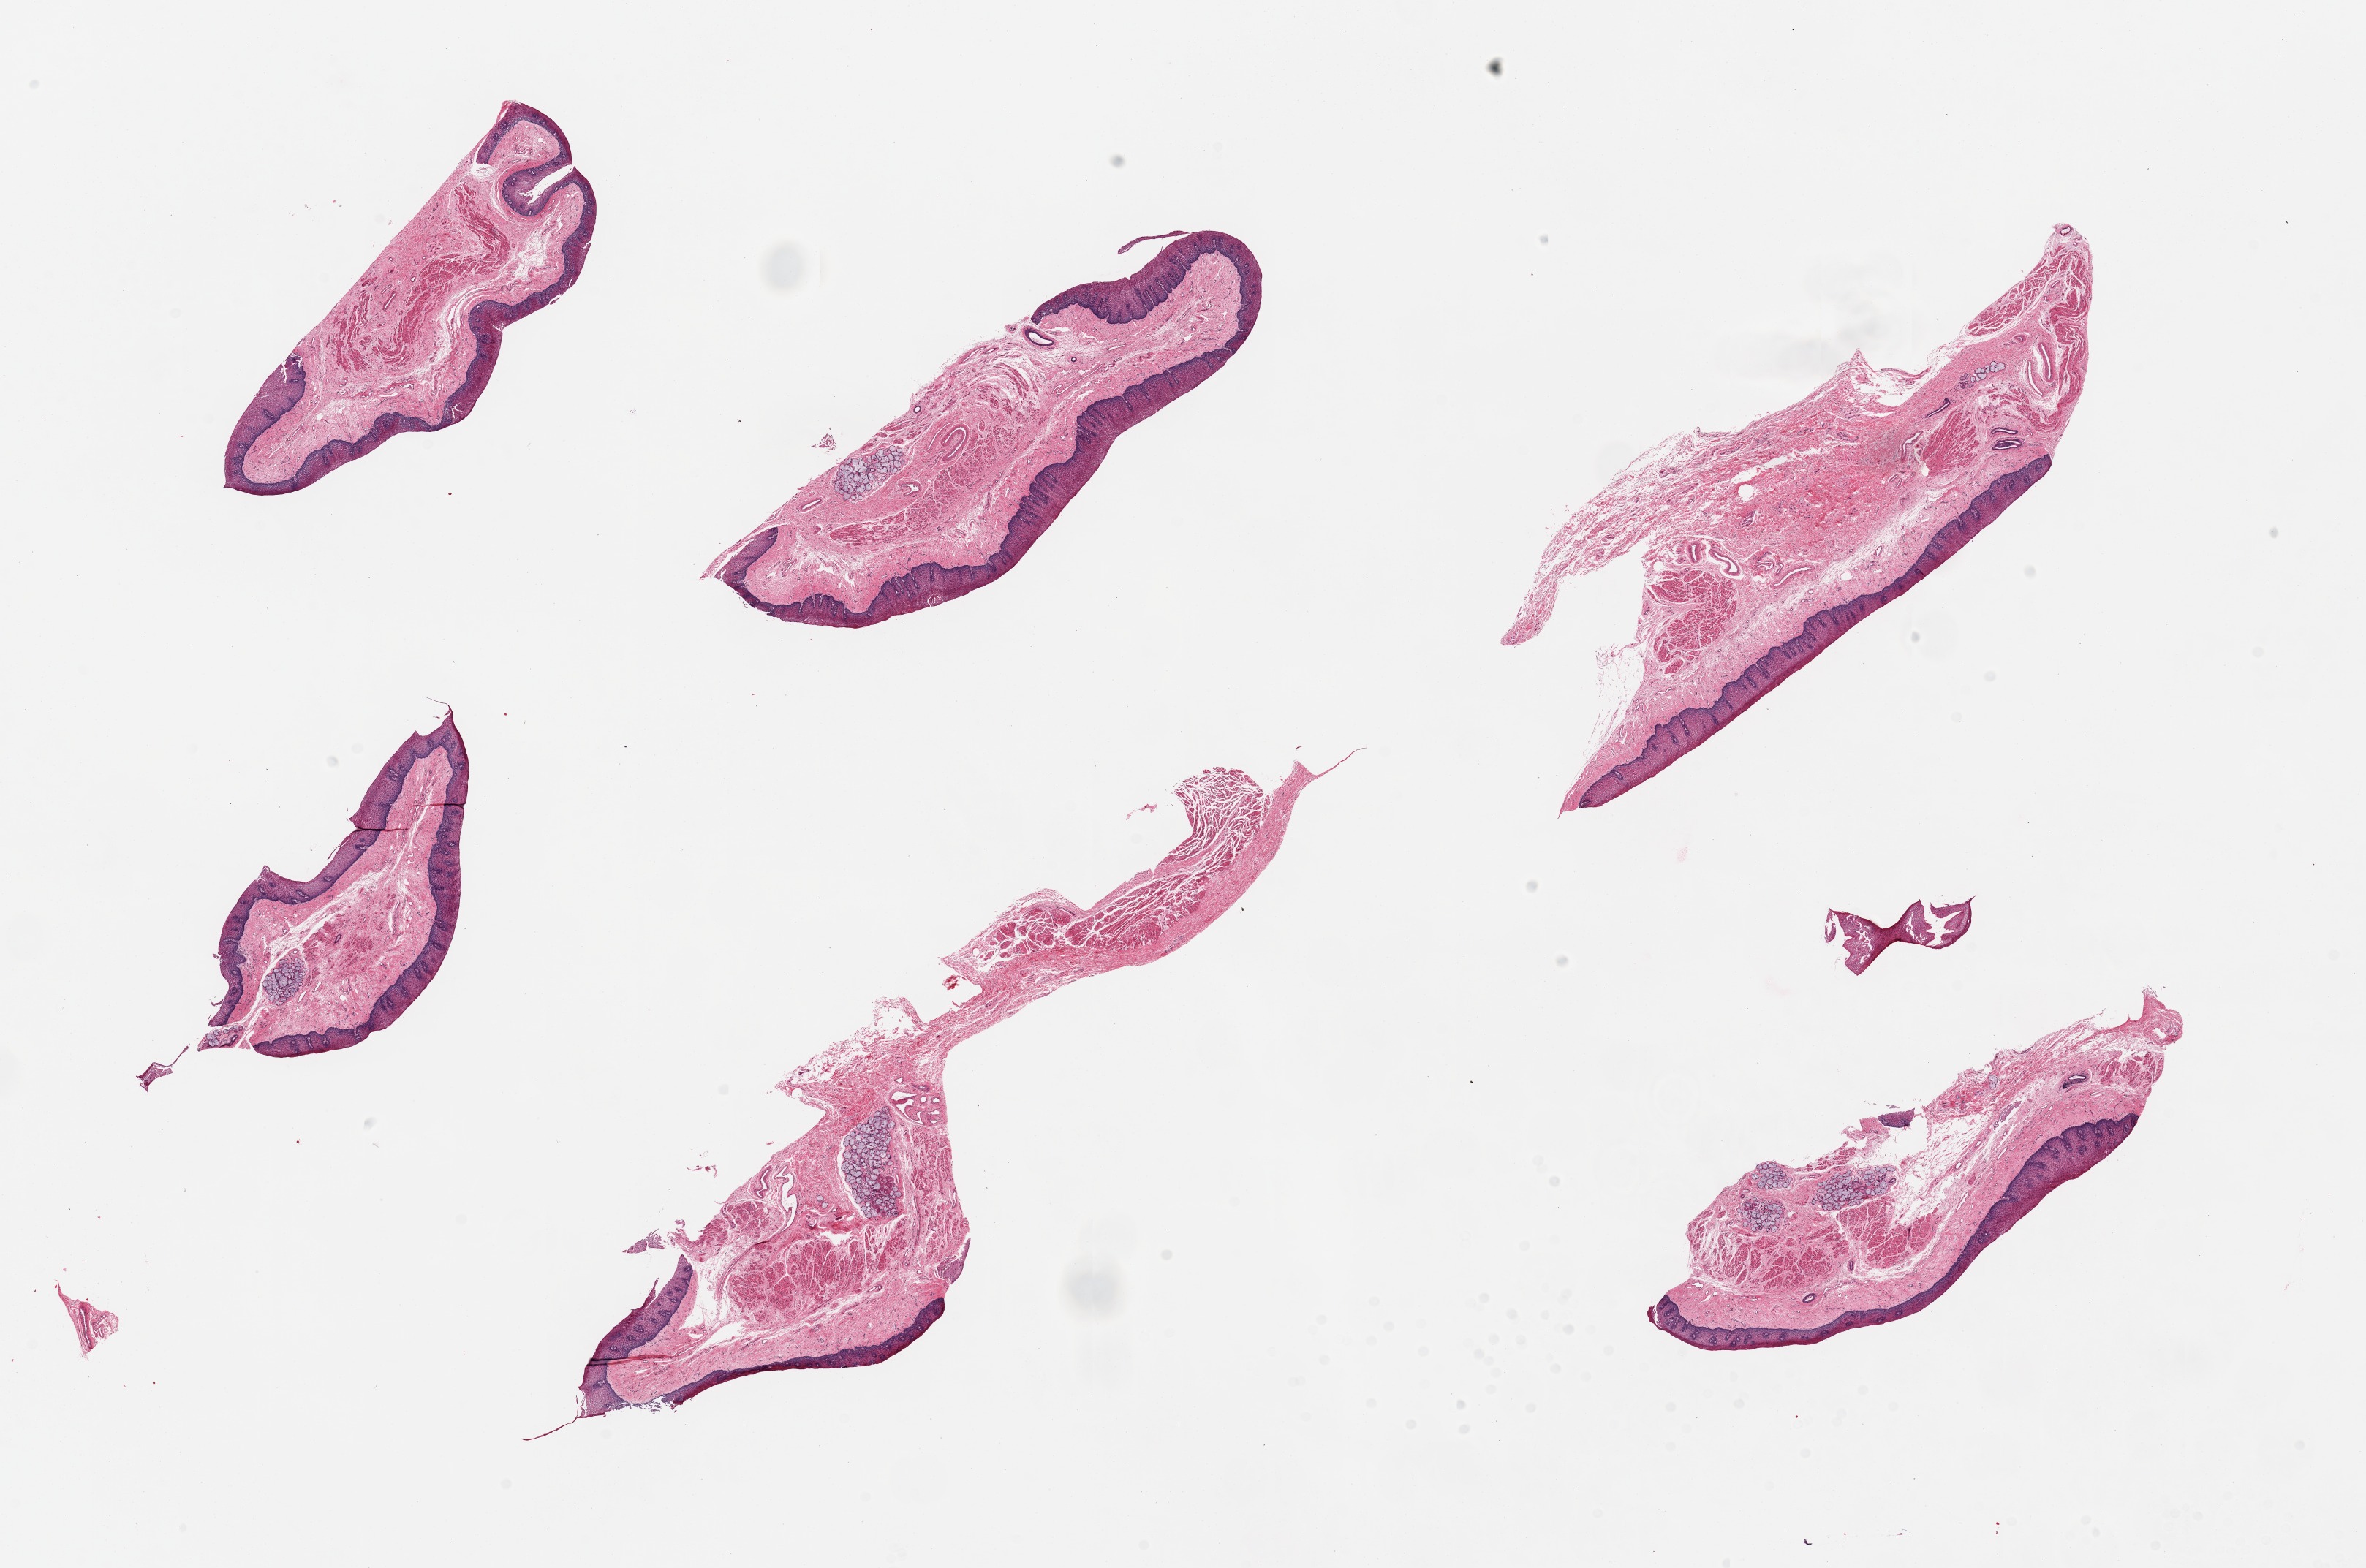
H&E whole-slide image — shown as a low-resolution overview of the whole scanned area (about 25.6 x 17.0 mm). PAXgene-fixed paraffin-embedded (PFPE) section. Sampled site (target tissue): esophageal mucous membrane. Donor tissue sample. Donor: female.
Review note (as recorded): 6 pieces, squamous mucosa is ~0.3mm, 15-20% of total thickness.